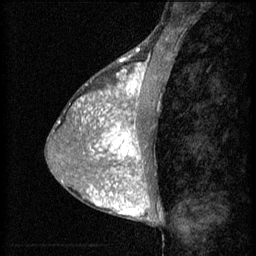
Breast MRI (dynamic contrast-enhanced), one sagittal slice. Slice 28 of 60 in the series (ordered by position). 3 images stored at this slice position (order not interpretable as contrast timing). 1.5 T. TE 4.2 ms, TR 8.2 ms. 2 mm slice thickness. 256 × 256 image matrix, field of view 180 × 180 mm. Patient: female, 38 years.
Annotated regions visible in this slice (semi-automatic segmentation, software-assisted and operator-edited):
- analysis volume of interest (the breast-tissue region the enhancement analysis was run in; not a lesion): bounding box [x1, y1, x2, y2] px = [95, 106, 155, 171]
- tumour enhancement mask (voxels above the 70 % enhancement threshold inside the analysis volume of interest): [95, 106, 147, 171]